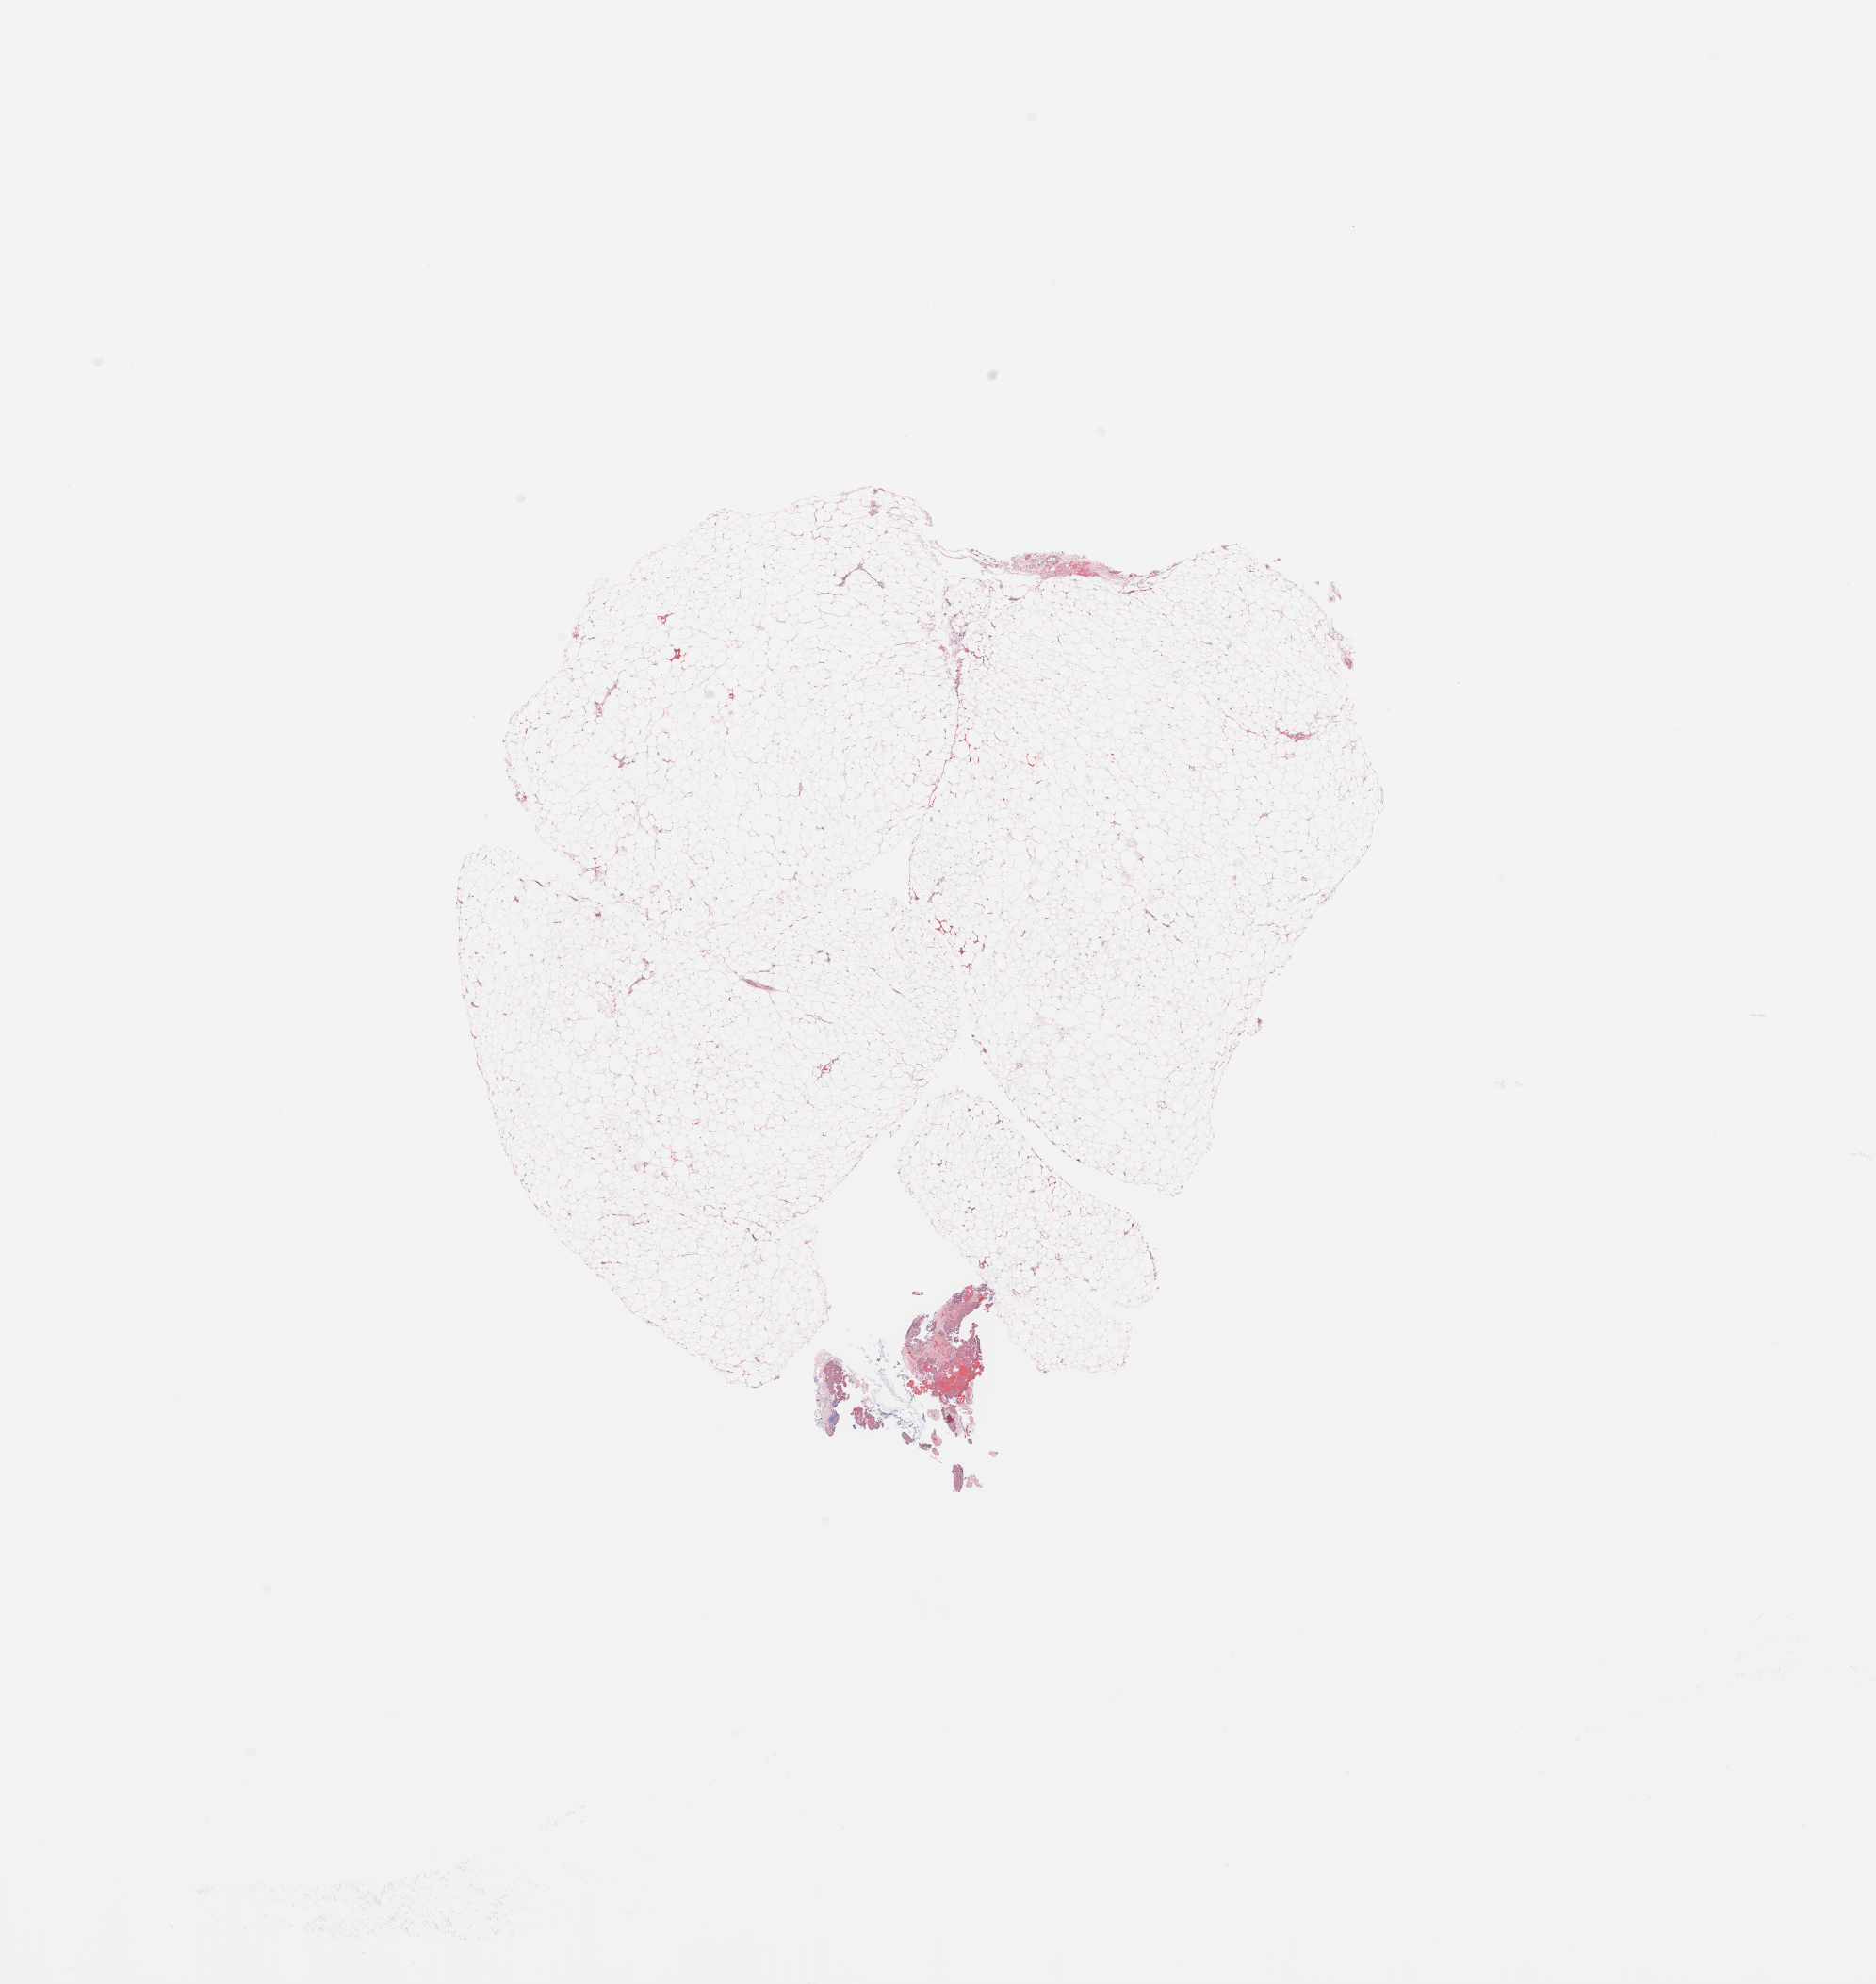
Digitized H&E tissue section (whole slide), low-resolution overview of the scanned area, about 15.8 x 16.7 mm (from a 20x scan), kidney, normal (non-tumour) tissue. Male, 53 y/o.
* this section: normal (non-tumour) tissue from the same patient
* patient diagnosis: Renal cell carcinoma, NOS